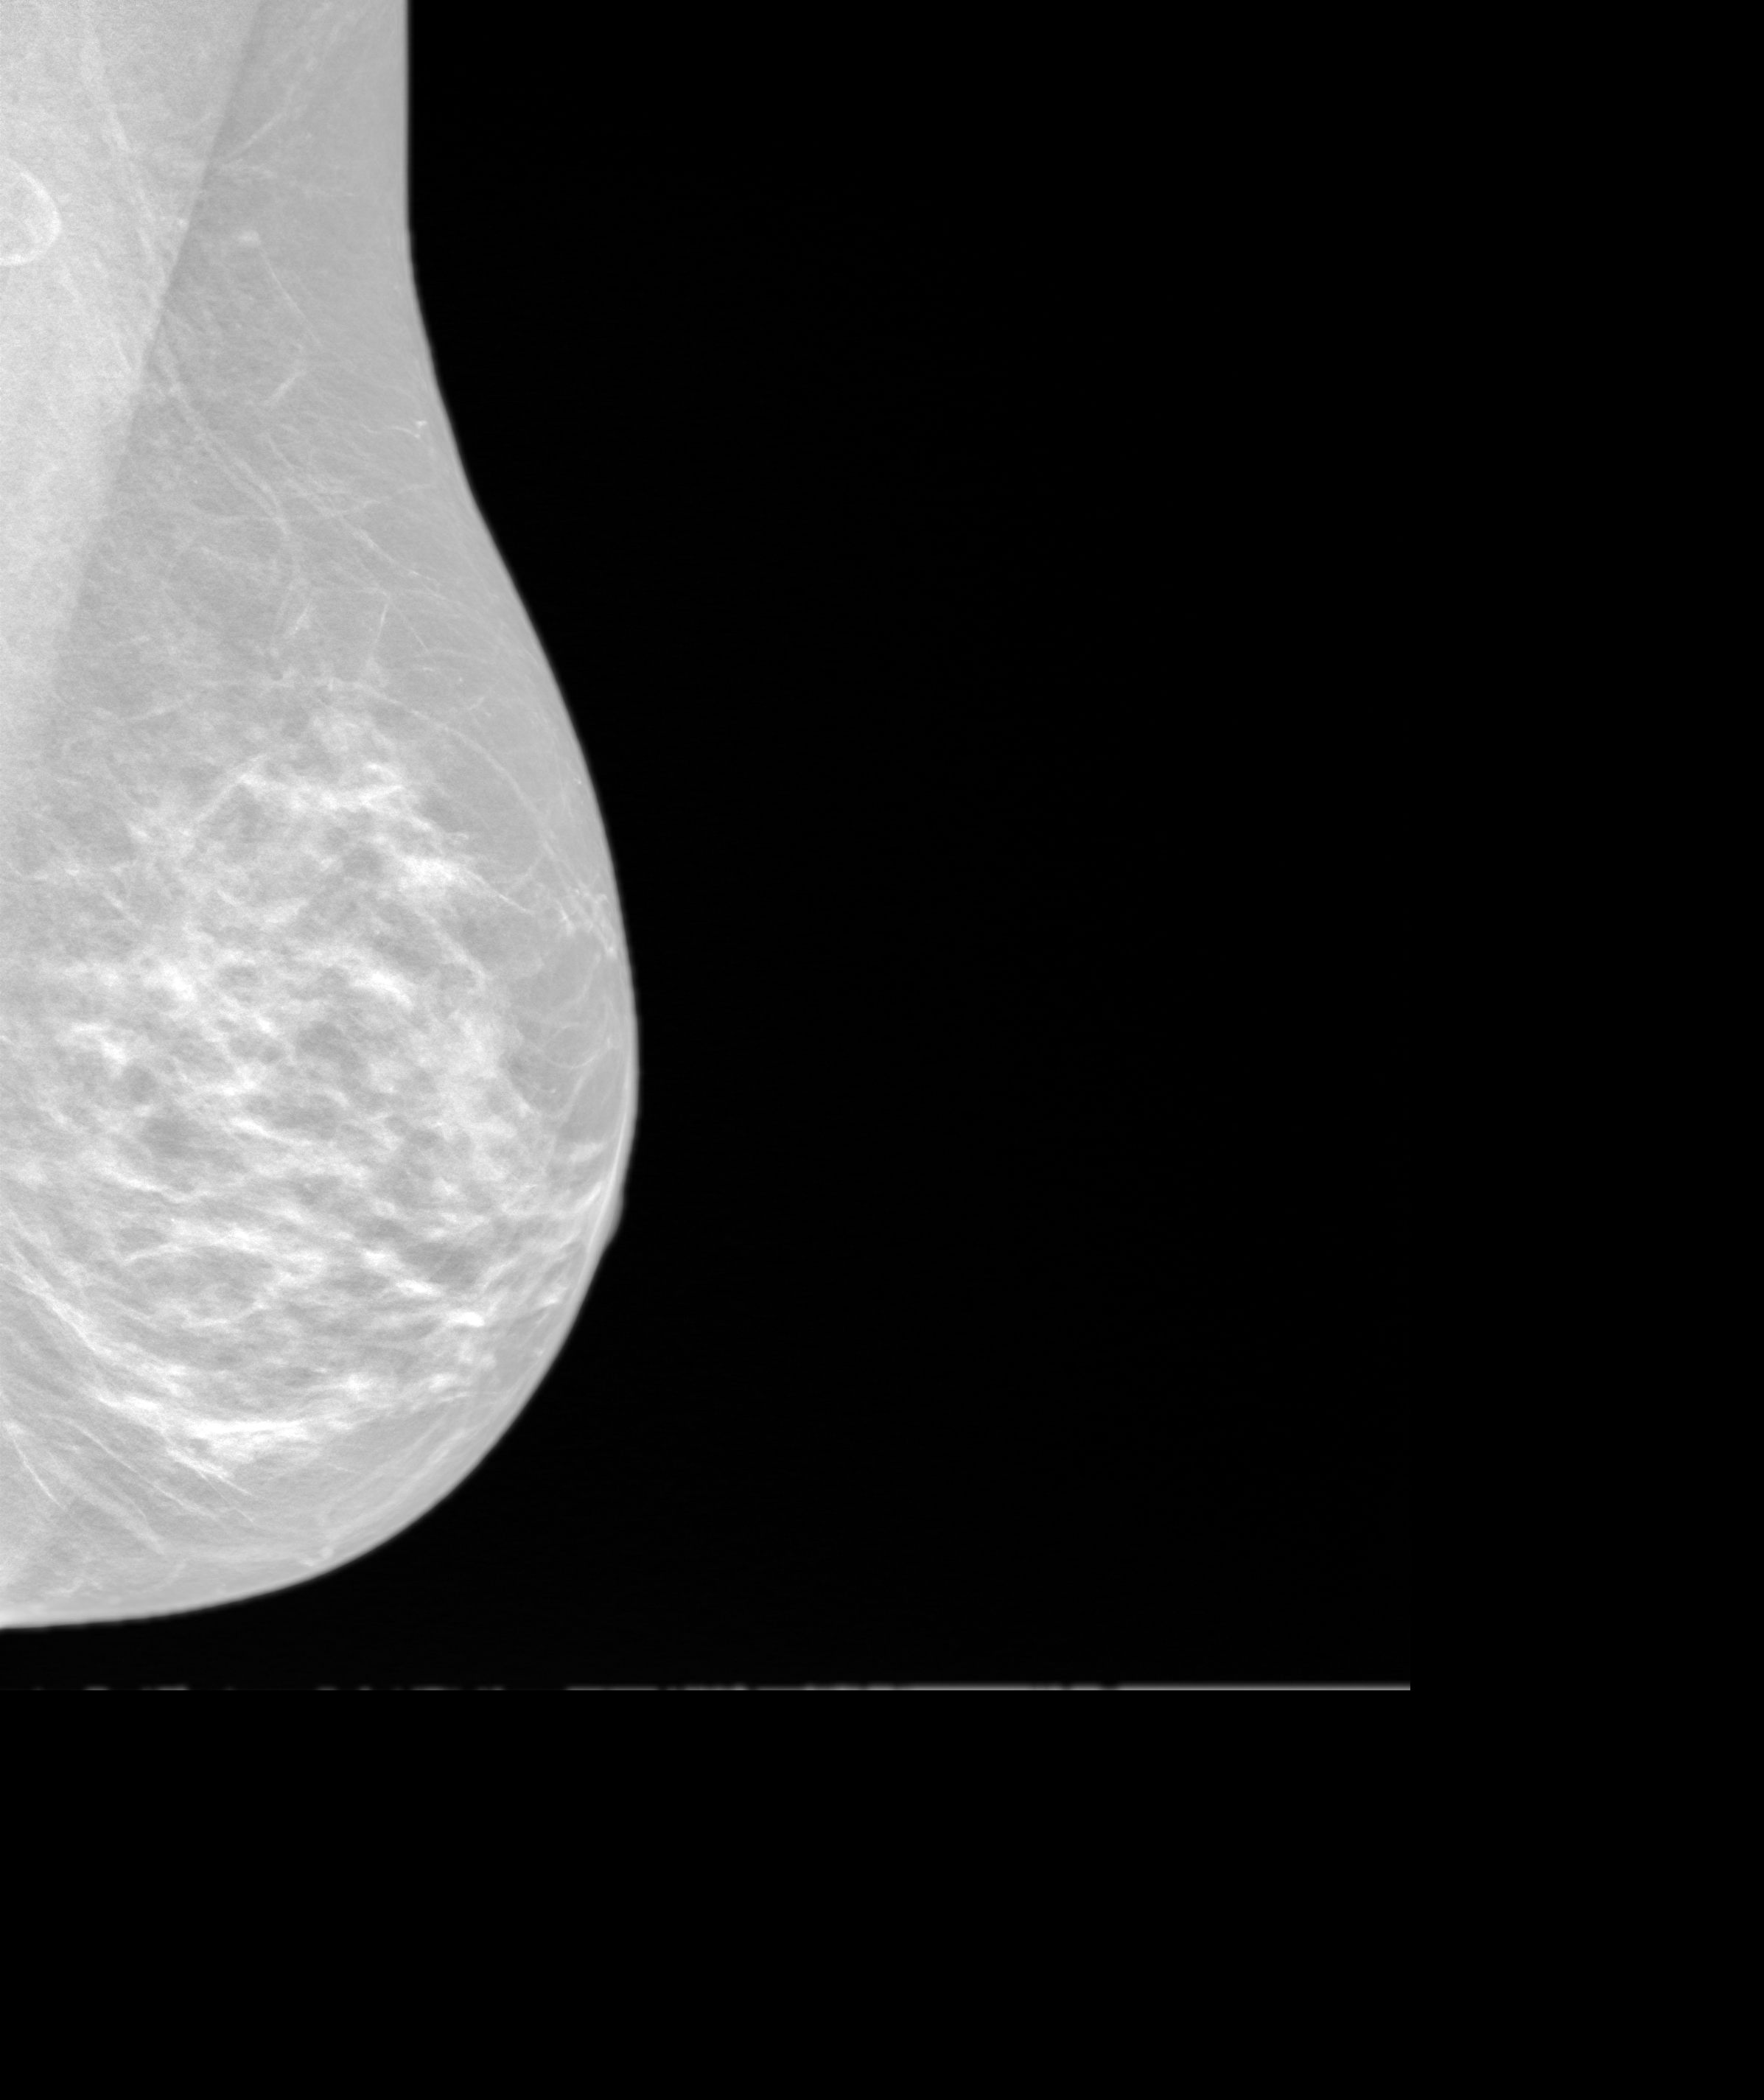
Screening examination. Female patient, age 59 years.
Image type: synthesized 2-D view from tomosynthesis. Breast: left. Projection: mediolateral oblique (MLO) view.